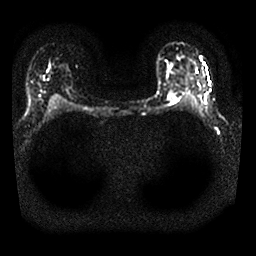
Breast MRI, one axial slice; position 19 of 25 along the scan axis; diffusion-weighted series; image 2 of 4 stored at this slice position (different b-values; order by instance number); 1.5 T; 256 × 256 image matrix. Female patient.
Structures marked on this image (outlined manually by an expert reader):
- tumour on diffusion-weighted imaging: box from (x=169, y=95) to (x=176, y=99) px